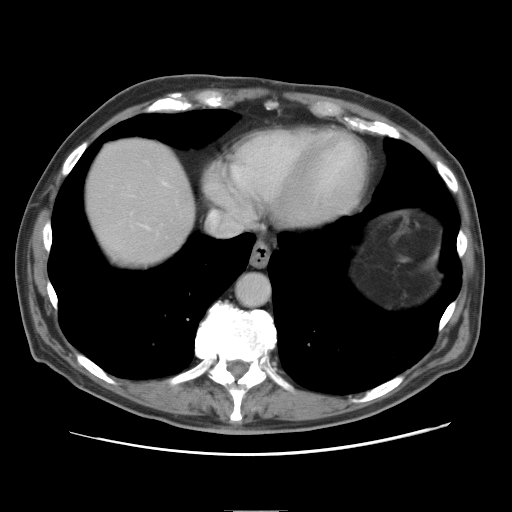
Contrast-enhanced abdominal CT, one axial slice; slice 74 of 89 in the series (ordered by position); intravenous contrast given; soft-tissue window (W 400 / L 40 HU); 512 × 512 image matrix. Male patient, age 69 years. From the clinical record (not read from this slice): diagnosis: colorectal cancer liver metastases, imaged before liver resection; multiple liver metastases: no; largest metastasis: 8.5 cm.
Outlined on this slice (expert manual segmentation):
- hepatic veins: bounding box [x1, y1, x2, y2] px = [146, 226, 149, 229]
- liver: [85, 140, 194, 263]
- planned liver remnant (the part of the liver to remain after resection): [86, 140, 194, 264]